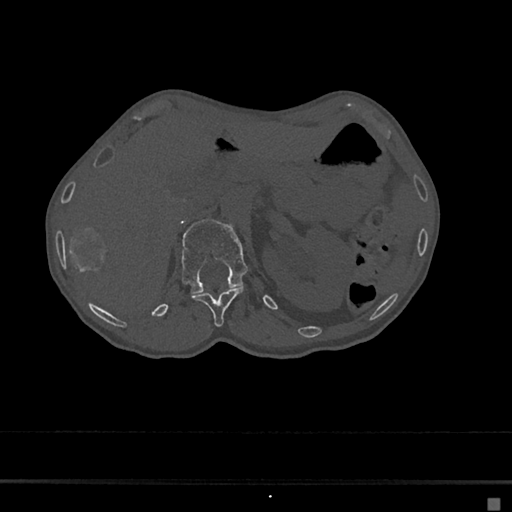
CT including the spine, one axial slice. Bone window (W 1800 / L 400 HU). 0.5 mm slice thickness. 512 × 512 image matrix. Patient: female, 68 years. Case-level facts recorded for this patient, not image findings: primary cancer: renal.
Structures marked on this image (semi-automatically segmented with operator editing):
- L1 vertebra: bounding box <181,219,248,294> (left, top, right, bottom; pixels)
- T12 vertebra: <192,287,244,327>